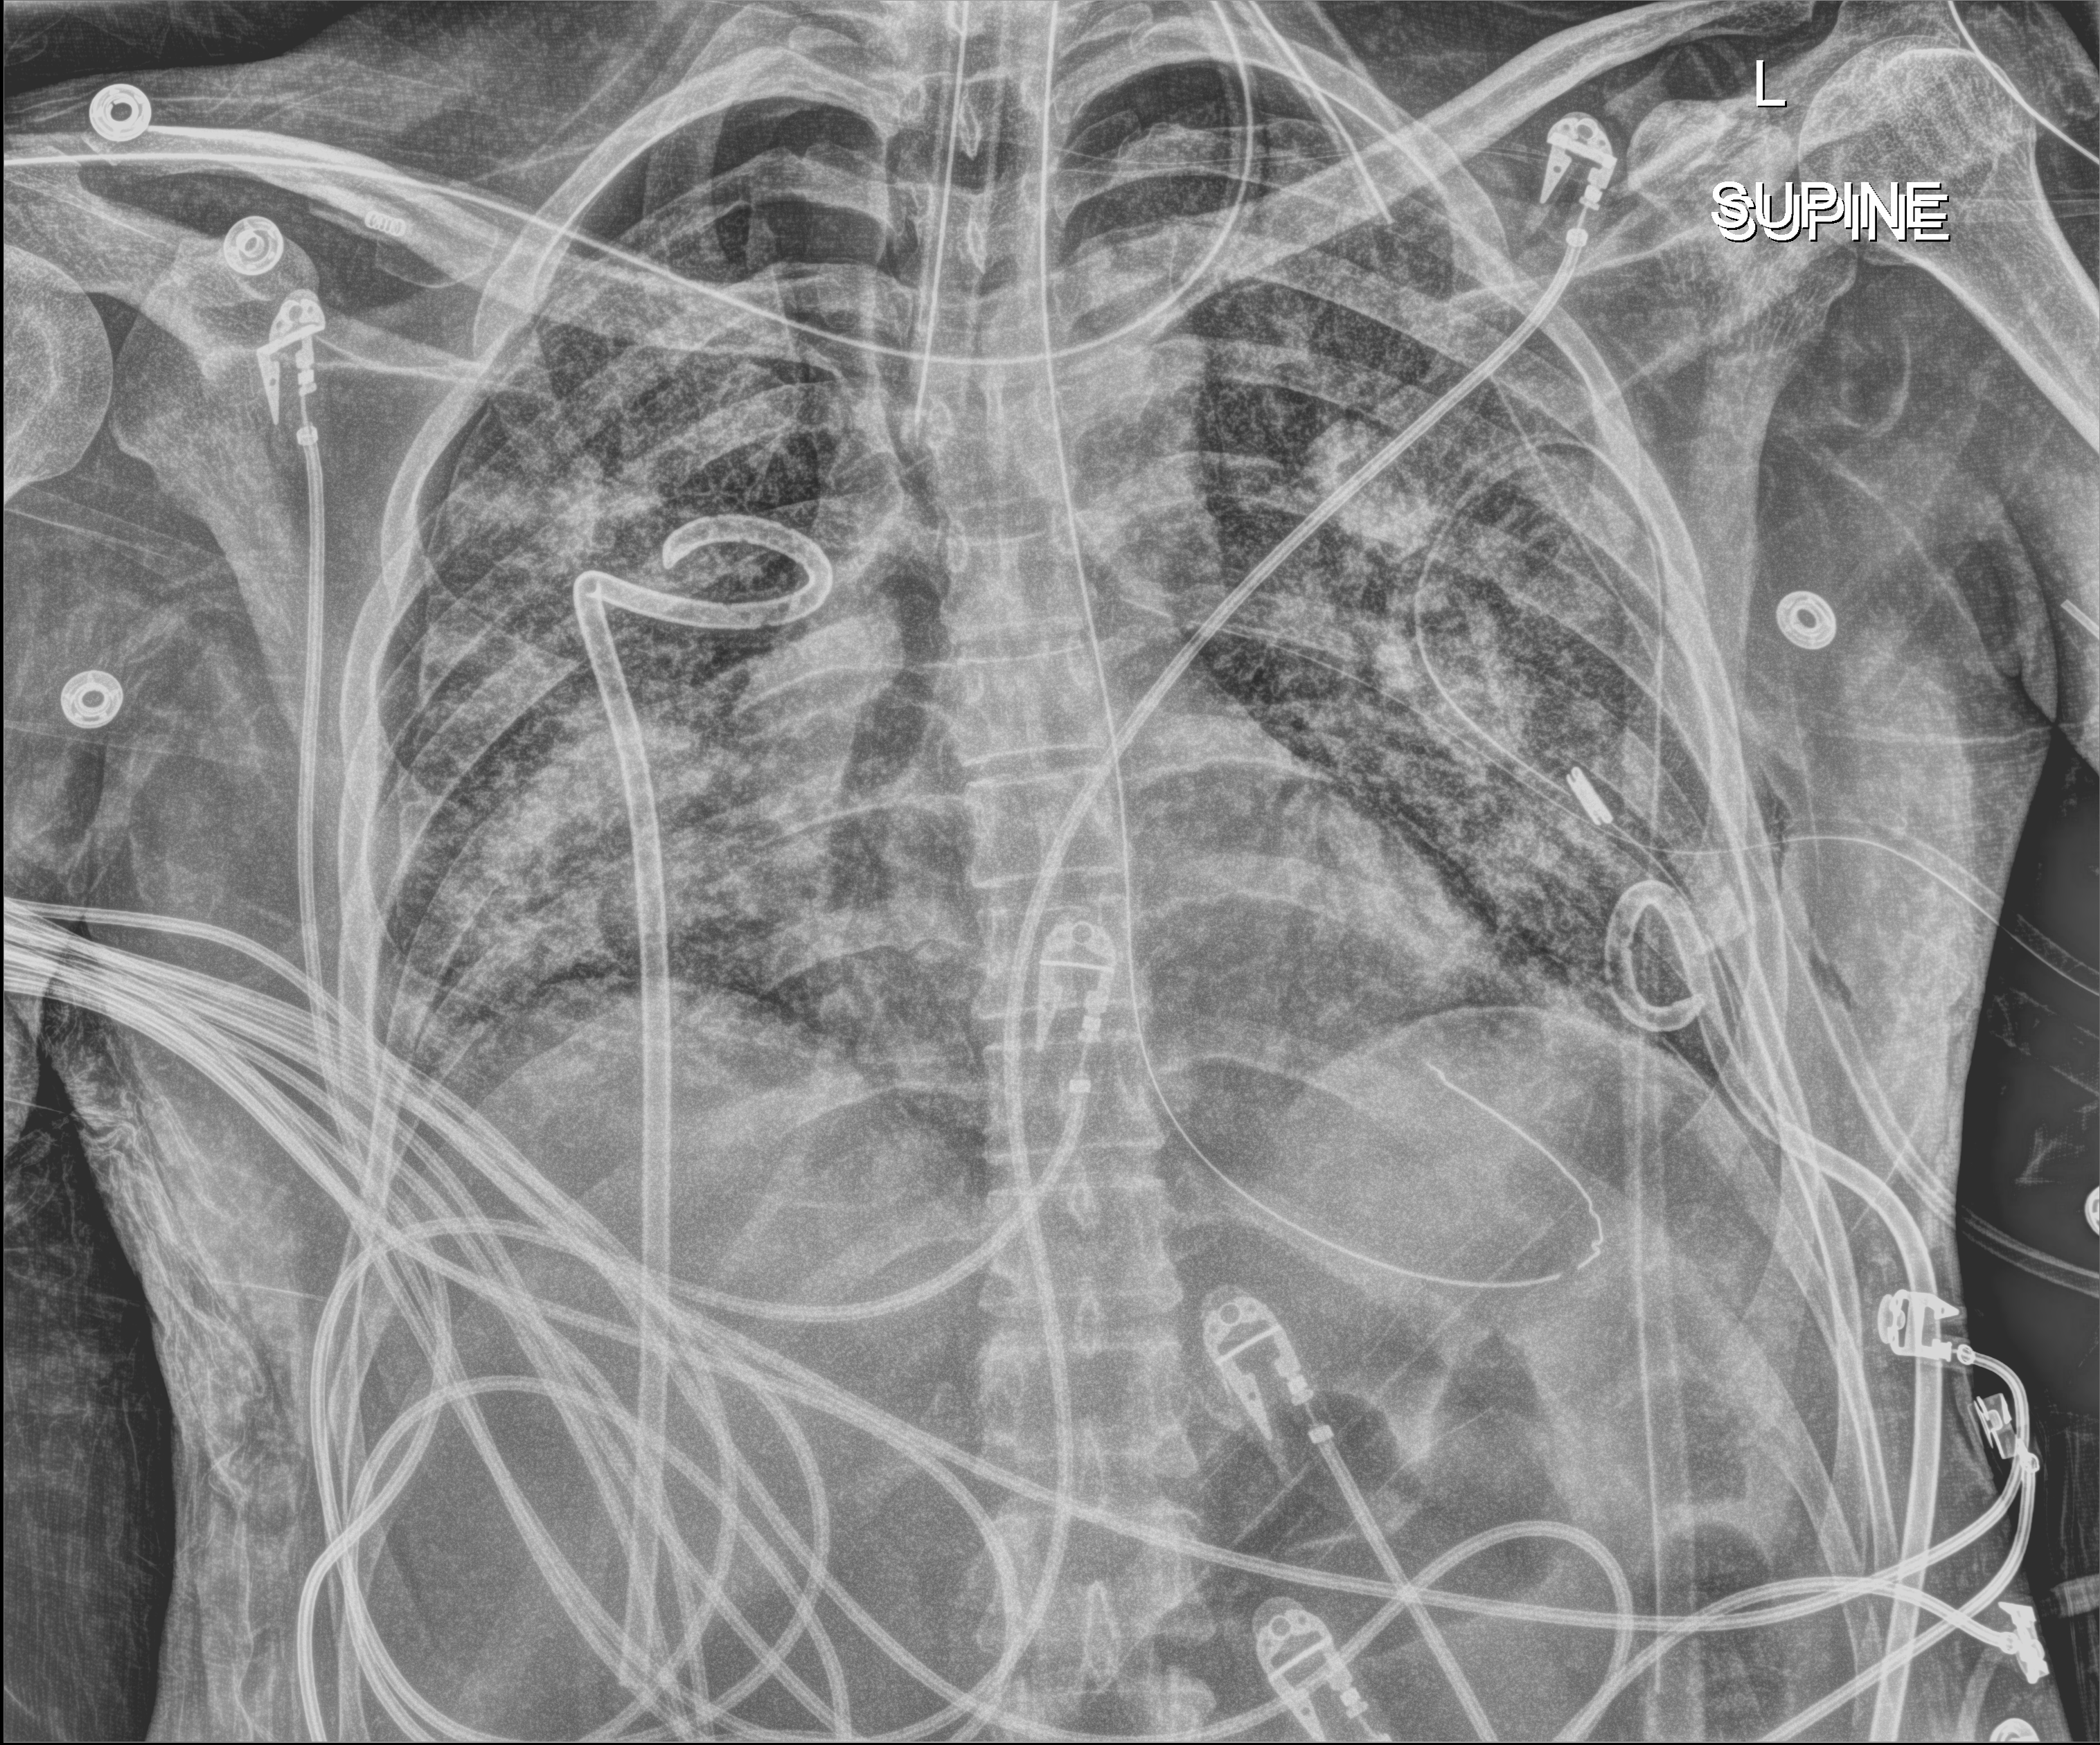
Chest radiograph (digital radiography); anteroposterior (AP) projection. Adult patient hospitalised with COVID-19, age 18–59 years.
Hospital-stay facts (about this admission, not read from this image; timing relative to this image not recorded): diabetes (admission record): no; COPD (admission record): no; admitted to intensive care during this hospital stay: yes.